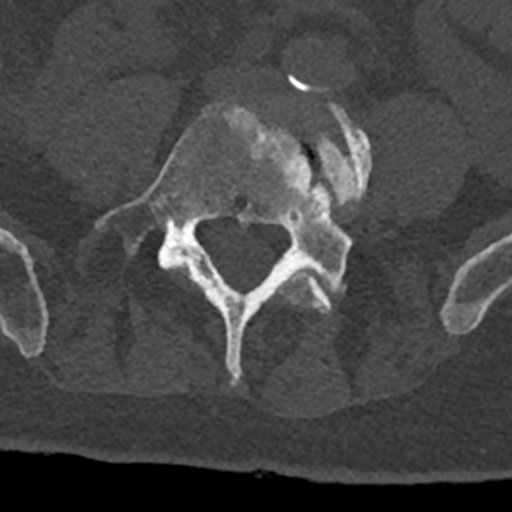
CT including the spine, one axial slice. Position 214 of 797 along the scan axis. Reconstruction kernel Br40s/3. Bone window (W 1800 / L 400 HU). 0.5 mm slice thickness. 512 × 512 image matrix, field of view 160 × 160 mm. Male patient, age 74 years. From the clinical record (not read from this slice): primary cancer: renal; vertebrae with lytic lesions (as recorded): T10, L1, L2, L3, L4, L5.
Annotated regions visible in this slice (semi-automatic segmentation, software-assisted and operator-edited):
- L4 vertebra: bounding box (x1, y1, x2, y2) in pixels: (176, 88, 372, 314)
- L5 vertebra: (95, 104, 351, 385)